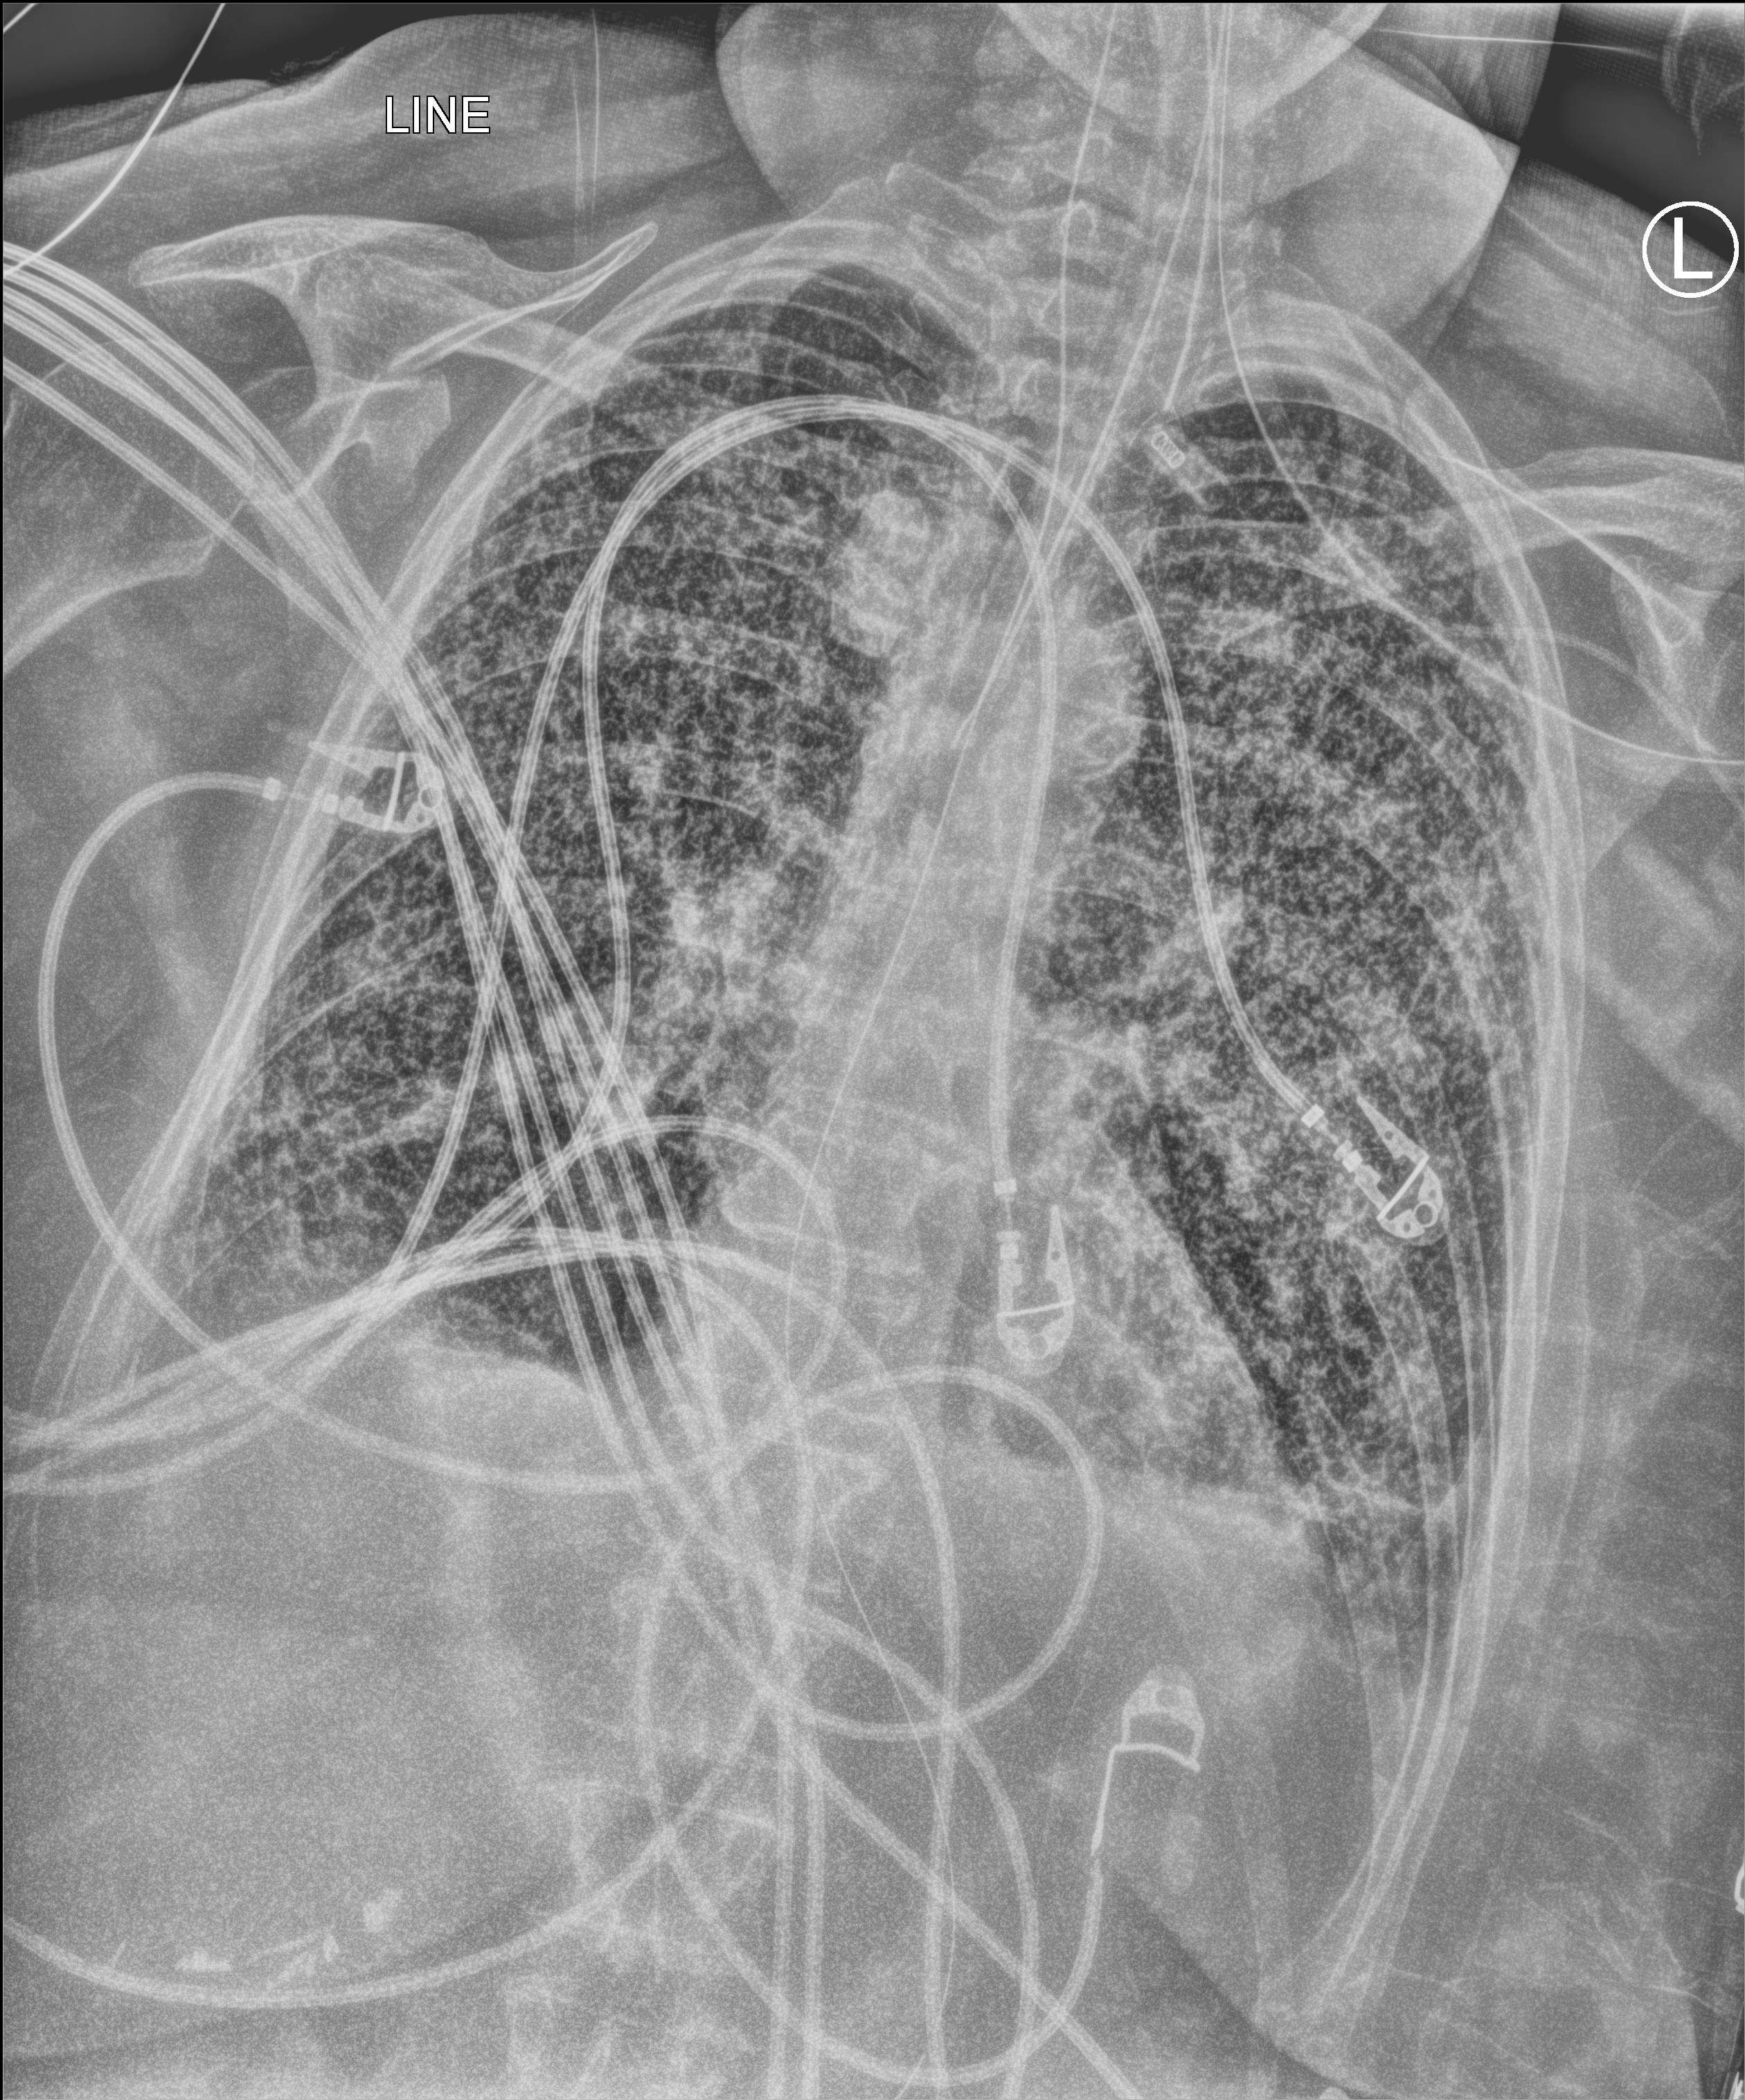
Bedside chest radiograph (computed radiography), anteroposterior (AP) projection. Patient hospitalised with COVID-19; female, aged 60–74 years.
Admission-level facts for this patient (not findings on this image; timing relative to this image not recorded): hypertension (admission record): no.